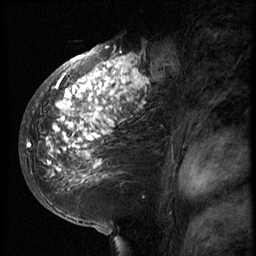
Breast MRI (dynamic contrast-enhanced), one sagittal slice. Position 40 of 66 along the scan axis. 3 images stored at this slice position (order not interpretable as contrast timing). 1.5 T. TE 4.2 ms, TR 8.9 ms. 2.5 mm slice thickness. 256 × 256 image matrix, field of view 200 × 200 mm. Female patient, age 39 years. From the clinical record (not read from this slice): setting: breast cancer imaged before/during neoadjuvant chemotherapy; receptor status: HER2-positive.
Structures marked on this image (semi-automatically segmented with operator editing):
- analysis volume of interest (the breast-tissue region the enhancement analysis was run in; not a lesion): bounding box <29,44,166,196> (left, top, right, bottom; pixels)
- tumour enhancement mask (voxels above the 140 % enhancement threshold inside the analysis volume of interest): <29,46,159,182>